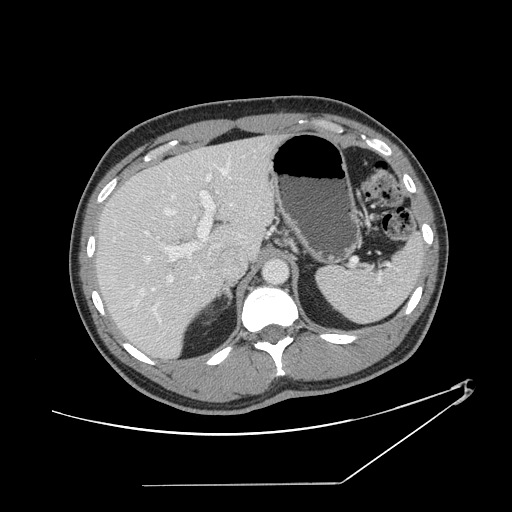
Contrast-enhanced abdominal CT, one axial slice. Position 96 of 152 along the scan axis. 120 kVp. Soft-tissue window (W 400 / L 40 HU). 2.5 mm slice thickness. 512 × 512 image matrix, field of view 432 × 432 mm. Male patient, age 45 years. Case-level facts recorded for this patient, not image findings: diagnosis: colorectal cancer liver metastases, imaged before liver resection.
Structures marked on this image (manually delineated by an expert):
- hepatic veins: bounding box (x1, y1, x2, y2) in pixels: (111, 156, 233, 296)
- liver: (98, 137, 276, 357)
- planned liver remnant (the part of the liver to remain after resection): (97, 154, 229, 357)
- portal vein (with intrahepatic branches): (145, 174, 215, 325)